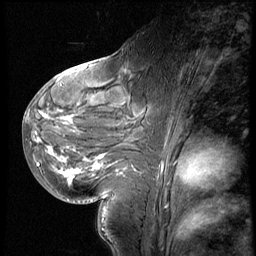
Breast MRI (dynamic contrast-enhanced), one sagittal slice. Slice 28 of 60 in the series (ordered by position). 3 images stored at this slice position (order not interpretable as contrast timing). 1.5 T. TE 4.2 ms, TR 8.9 ms. 2.5 mm slice thickness. 256 × 256 image matrix. Female patient, age 29 years. Case-level facts recorded for this patient, not image findings: setting: breast cancer imaged before/during neoadjuvant chemotherapy.
Structures marked on this image (semi-automatic segmentation, software-assisted and operator-edited):
- analysis volume of interest (the breast-tissue region the enhancement analysis was run in; not a lesion): bounding box [x1, y1, x2, y2] px = [29, 57, 157, 200]
- tumour enhancement mask (voxels above the 140 % enhancement threshold inside the analysis volume of interest): [37, 113, 106, 182]